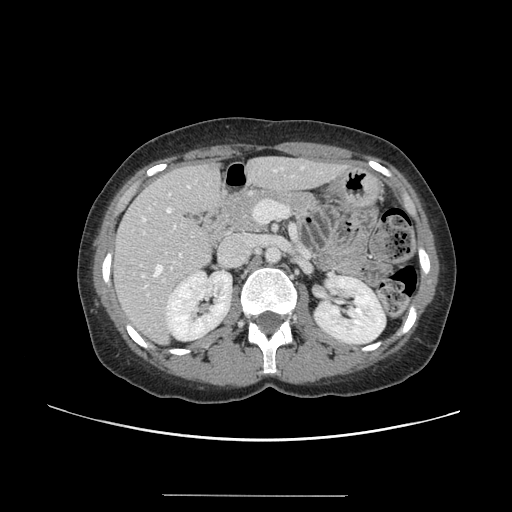
Contrast-enhanced abdominal CT, one axial slice. Position 70 of 144 along the scan axis. 120 kVp. Intravenous contrast given. Soft-tissue window (W 400 / L 40 HU). 2.5 mm slice thickness. 512 × 512 image matrix, field of view 380 × 380 mm. Female patient, age 53 years. From the clinical record (not read from this slice): diagnosis: colorectal cancer liver metastases, imaged before liver resection; multiple liver metastases: yes; largest metastasis: 1.1 cm; disease in both lobes: no.
Annotated regions visible in this slice (outlined manually by an expert reader):
- hepatic veins: bounding box <142,170,276,277> (left, top, right, bottom; pixels)
- liver: <115,159,339,342>
- planned liver remnant (the part of the liver to remain after resection): <115,159,323,303>
- portal vein (with intrahepatic branches): <140,200,289,296>